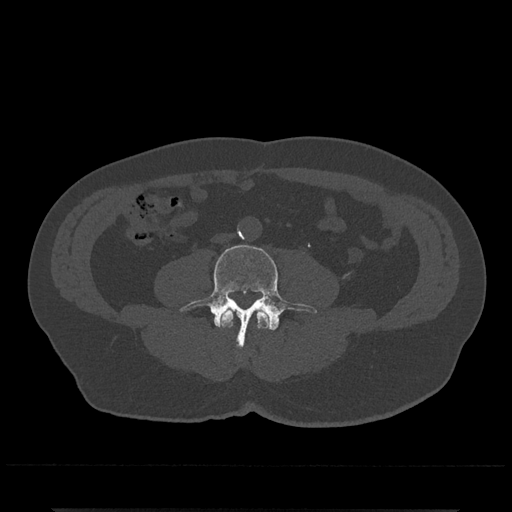
CT including the spine, one axial slice; position 164 of 797 along the scan axis; reconstruction kernel Br40s/3; 120 kVp; bone window (W 1800 / L 400 HU); 0.5 mm slice thickness; 512 × 512 image matrix, field of view 393 × 393 mm. Patient: male, 67 years. From the clinical record (not read from this slice): primary cancer: prostate.
Structures marked on this image (semi-automatically segmented with operator editing):
- L3 vertebra: bounding box [x1, y1, x2, y2] px = [220, 309, 270, 329]
- L4 vertebra: [179, 244, 317, 348]